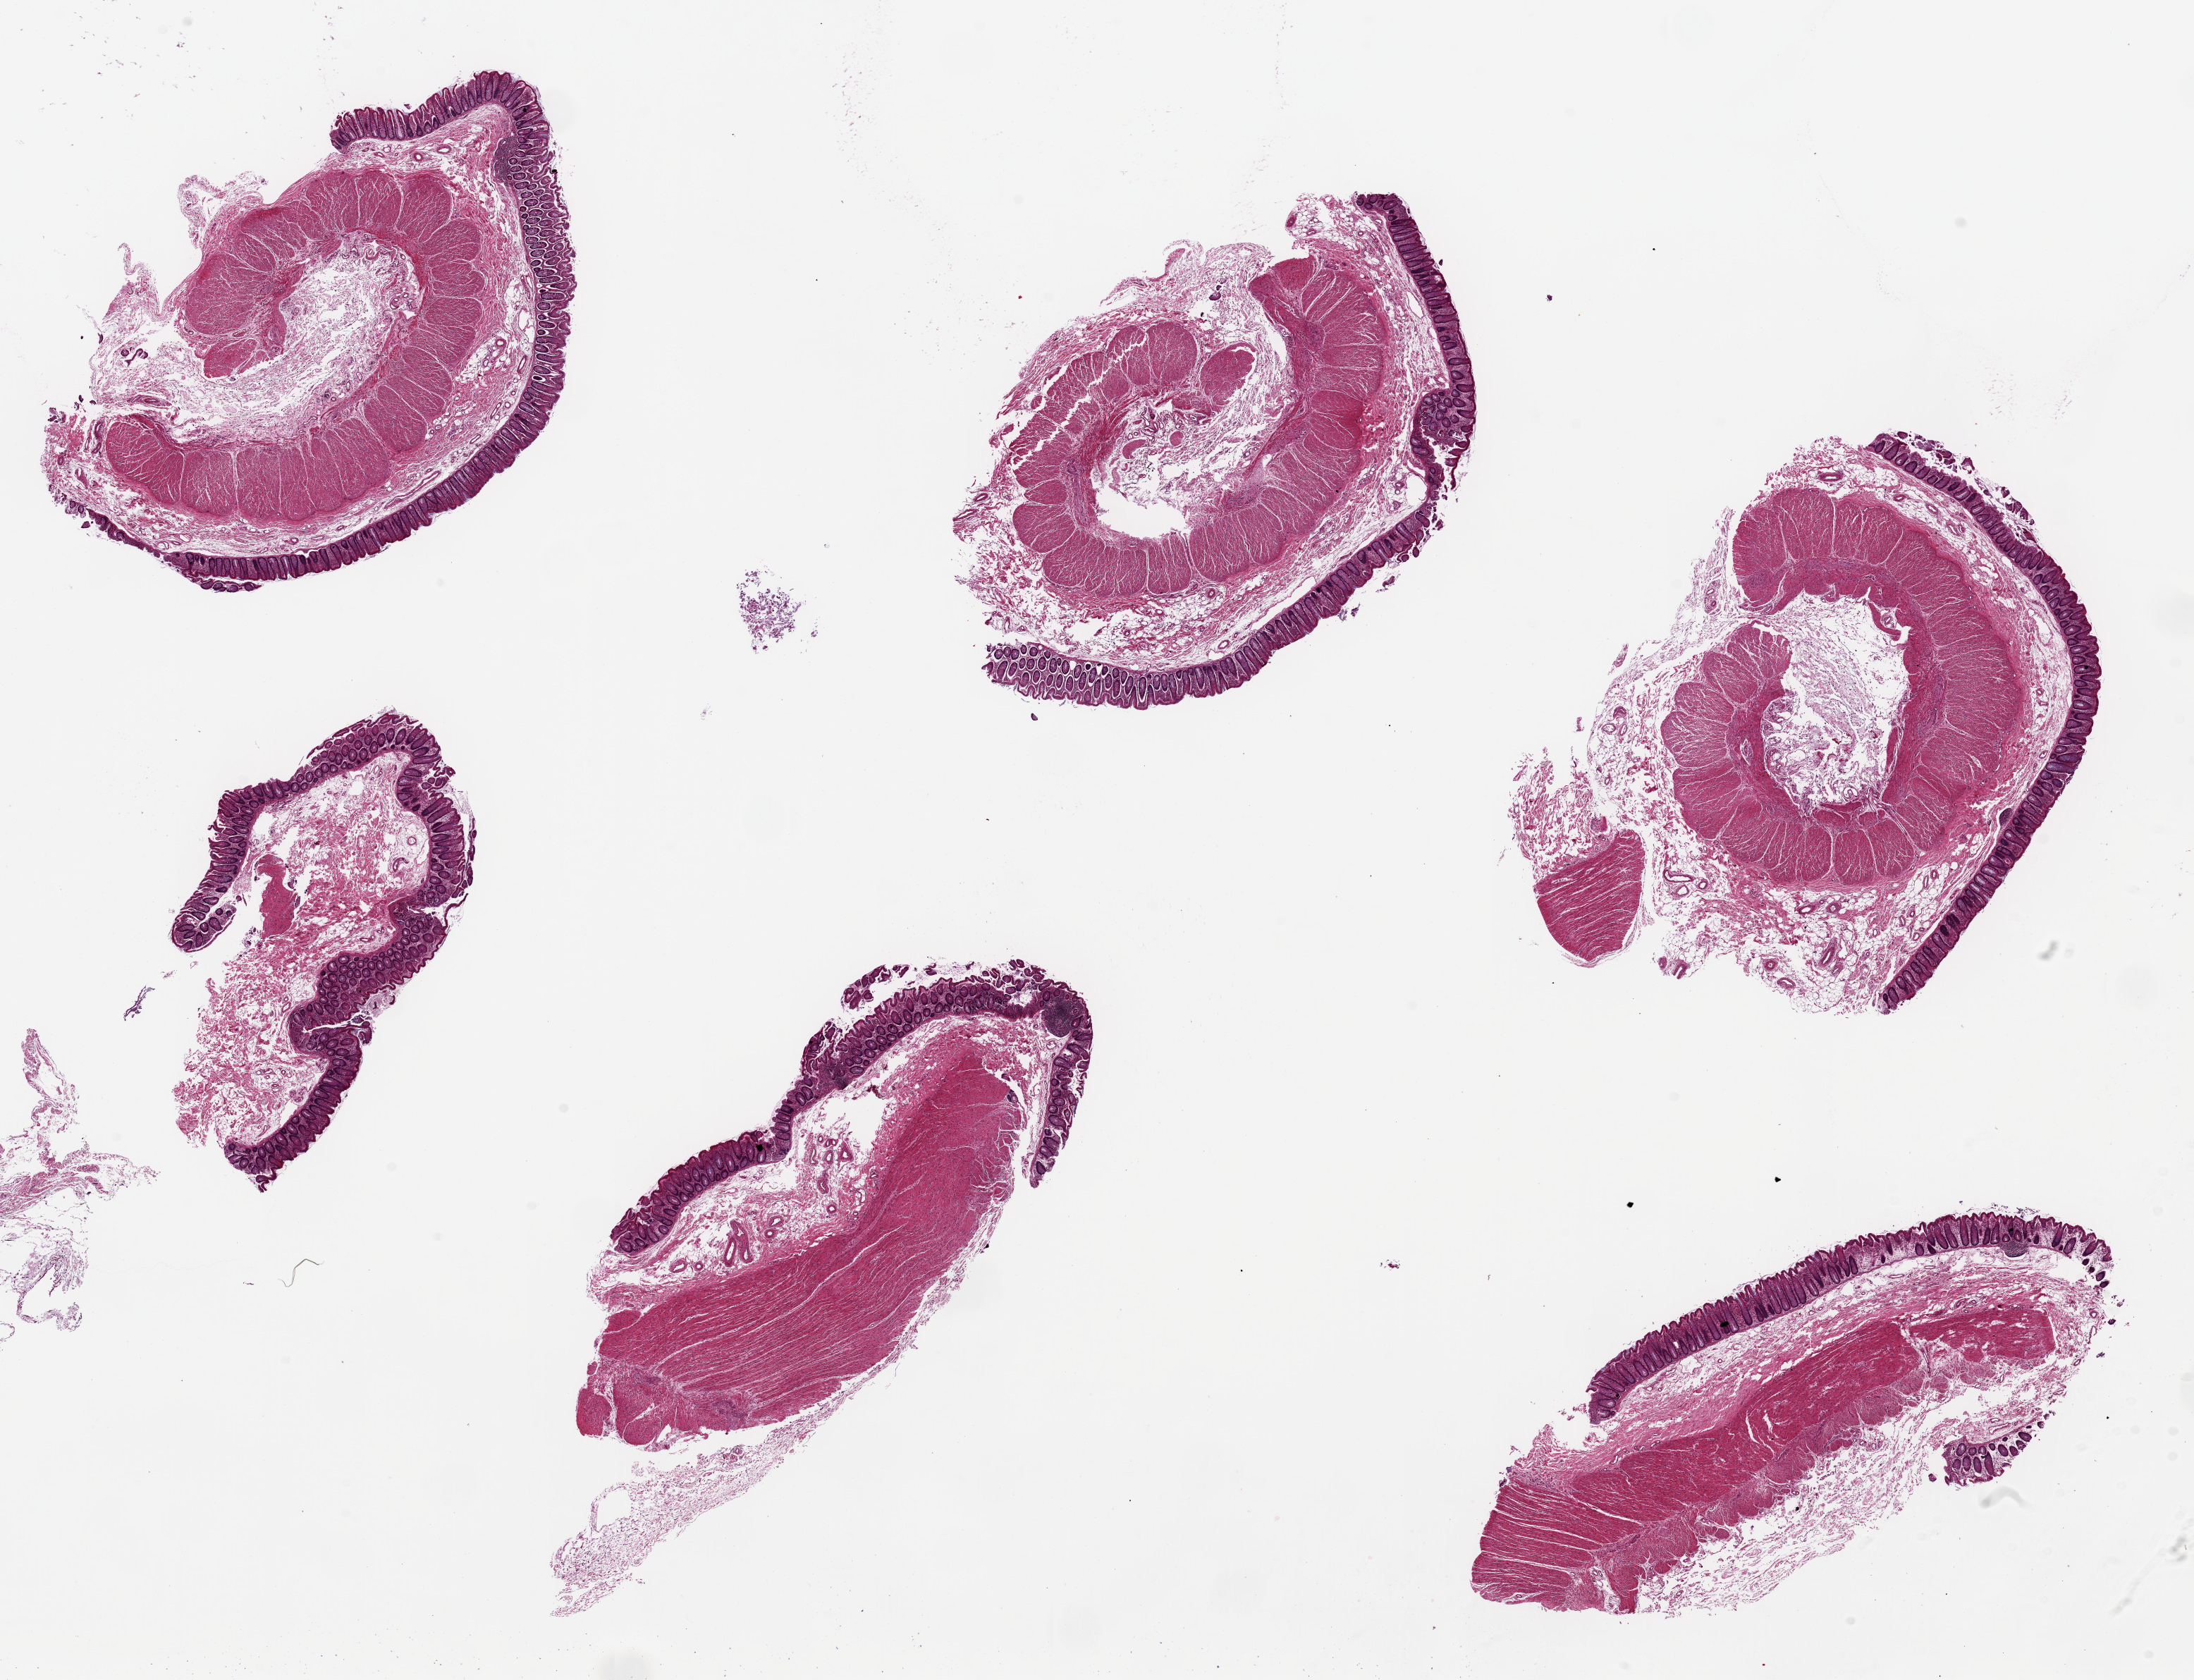
Haematoxylin and eosin whole-slide image, brightfield, shown as a low-resolution overview of the whole scanned area (about 24.6 x 18.8 mm); PAXgene-fixed, paraffin-embedded tissue; section of transverse colon (target tissue); tissue donor sample. Donor sex: male.
Reviewer comment on this tissue sample: 6 pieces ~7x4mm, mucosa is ~10% of thickness, well preserved.